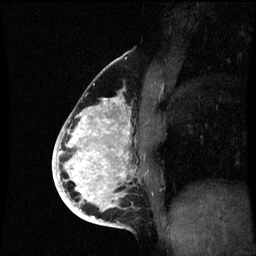
Breast MRI (dynamic contrast-enhanced), one sagittal slice; slice 32 of 60 in the series (ordered by position); dynamic contrast-enhanced series, image 2 of 3 at this slice position (ordered by acquisition); 1.5 T; TE 4.2 ms, TR 8.9 ms; 256 × 256 image matrix, field of view 200 × 200 mm. Patient: female, 35 years. Case-level facts recorded for this patient, not image findings: setting: breast cancer imaged before/during neoadjuvant chemotherapy; receptor status: HR-positive, HER2-negative.
Outlined on this slice (semi-automatic segmentation, software-assisted and operator-edited):
- analysis volume of interest (the breast-tissue region the enhancement analysis was run in; not a lesion): bounding box (x1, y1, x2, y2) in pixels: (66, 96, 149, 215)
- tumour enhancement mask (voxels above the 70 % enhancement threshold inside the analysis volume of interest): (66, 98, 131, 215)